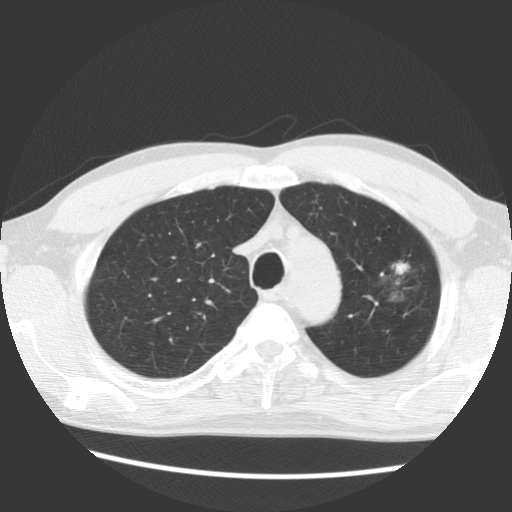
Chest CT (low-dose screening protocol), one axial image, baseline annual screen, lung window (W 1500 / L -600 HU), 2.5 mm slice thickness, standard (soft-tissue) reconstruction kernel (STANDARD), slice 107 of 138 in the series. Male participant, aged 61 years at enrolment. Former smoker at enrolment.
Lesion marked by an expert reader, bounding box (x1, y1, x2, y2) in pixels: (350, 243, 436, 325). The exam's reader record, not a measurement of the box and not confirmed to be the same lesion: non-calcified nodule or mass ≥4 mm, left upper lobe, 17 × 14 mm, soft tissue attenuation. Official screen result: positive, change unspecified: nodule(s) >= 4 mm or enlarging nodule(s), mass(es), or other non-specific abnormalities suspicious for lung cancer. Later outcome: lung cancer diagnosed 1061 days after this screen — bronchiolo-alveolar adenocarcinoma, NOS, left upper lobe, well differentiated (G1), stage IB (AJCC 6th edition), 44 mm at pathology.